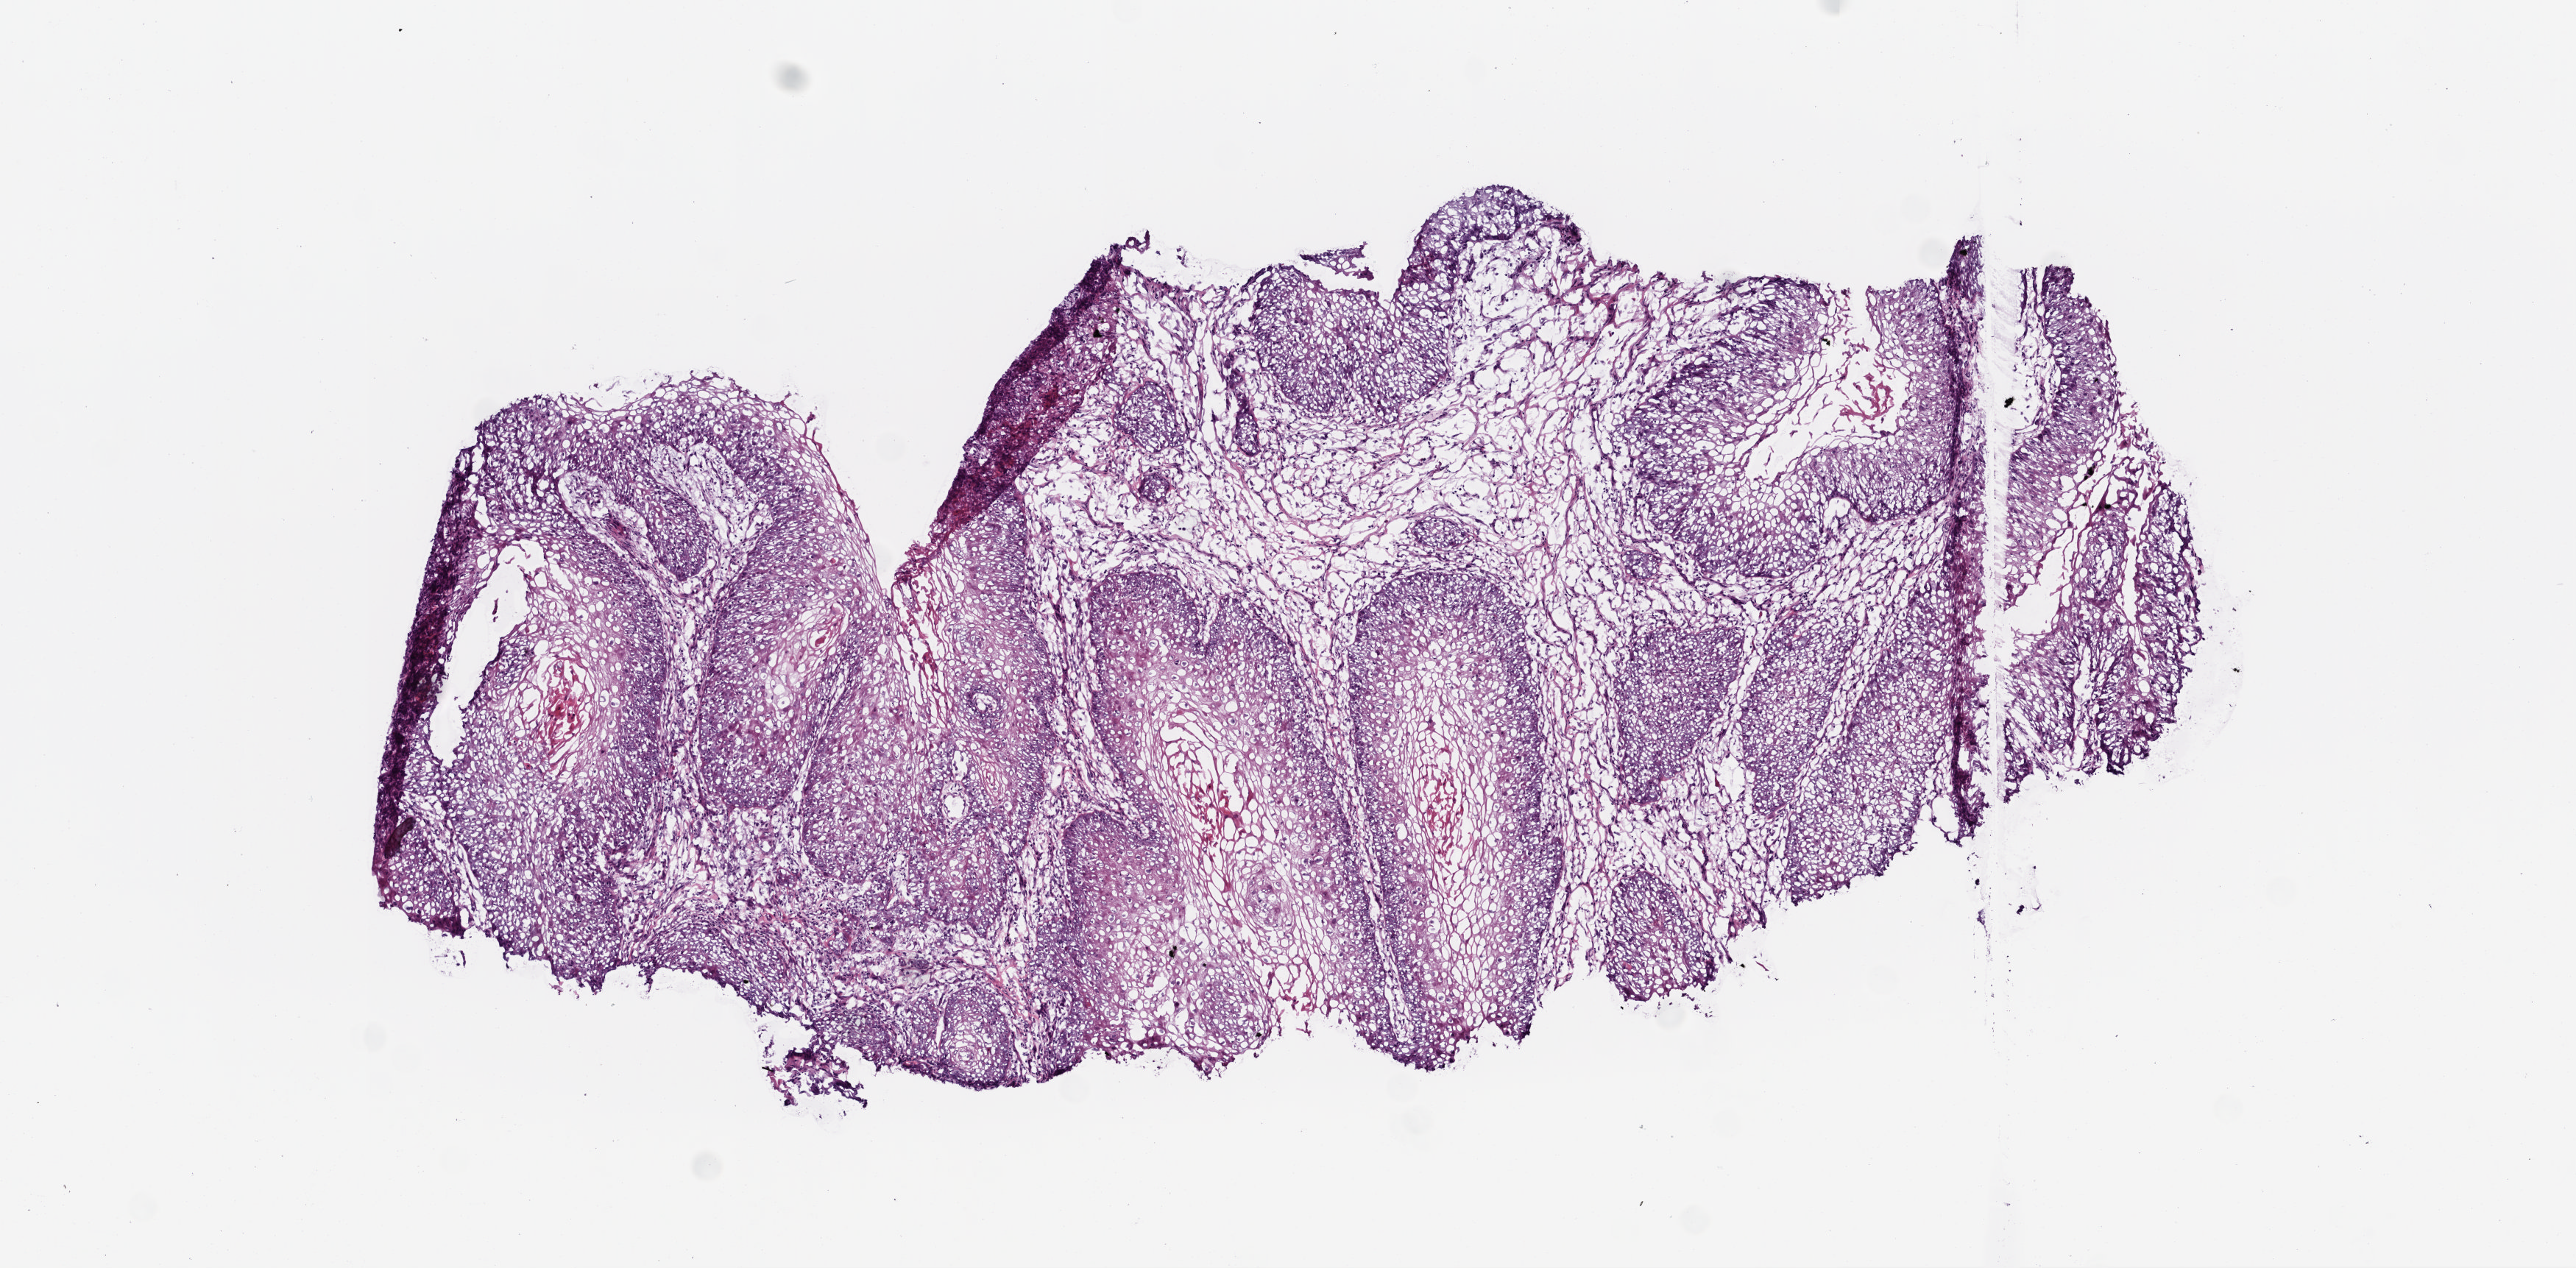
Whole-slide histology image, Hematoxylin and eosin (H&E) stained, low-resolution overview of the scanned area, about 7.0 x 3.5 mm. Frozen section. Primary tumour sample from the head and neck. Male patient; age at initial diagnosis 87 years. Histologic grade: G2 (moderately differentiated). Slide review estimates, as recorded: tumour cells 99%, tumour nuclei 80%, necrosis 1%. Inflammatory infiltration, as recorded: lymphocyte infiltration 10%.
AJCC pathologic stage: IVA (6th edition). Histologic diagnosis: Squamous cell carcinoma, NOS (cheek mucosa).